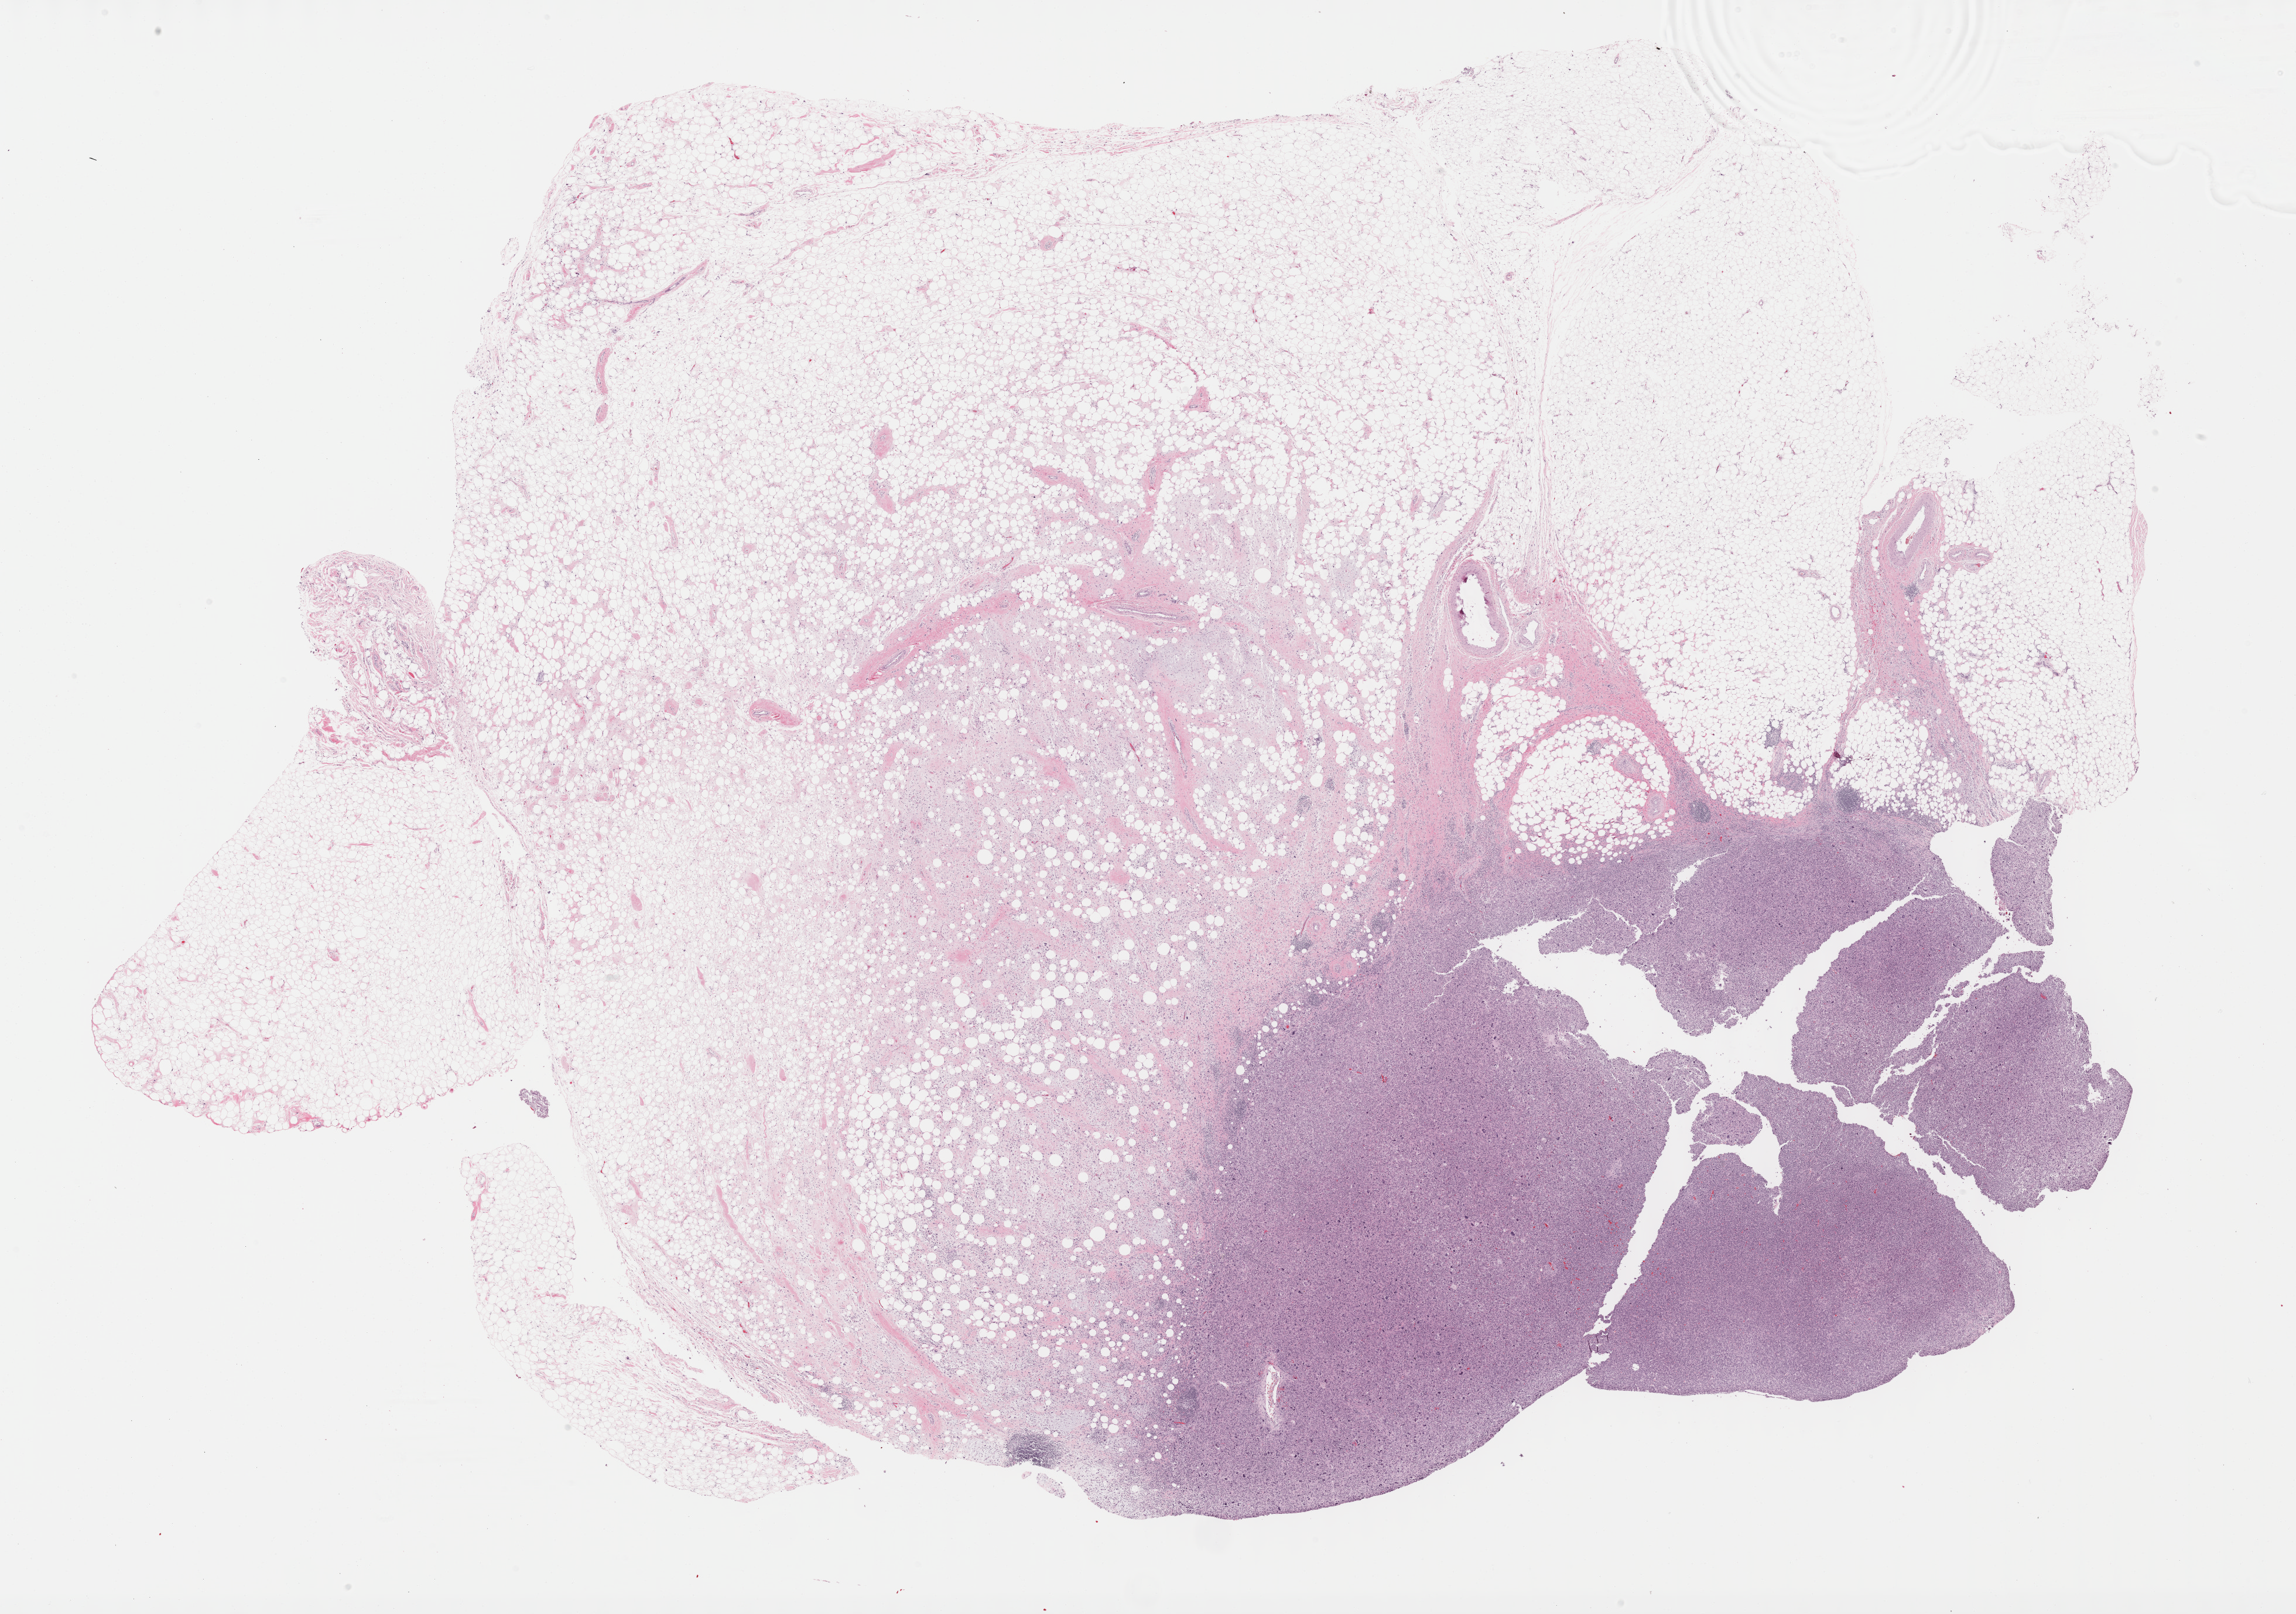
Whole-slide histology image, Hematoxylin and eosin (H&E) stained — whole scanned area (about 31.7 x 22.3 mm, slide scanned at 40x) shown as a low-resolution overview, FFPE section, primary tumour sample from the retroperitoneum and peritoneum. Patient: female, age at initial diagnosis 63 years.
* pathologic diagnosis: Dedifferentiated liposarcoma (retroperitoneum)